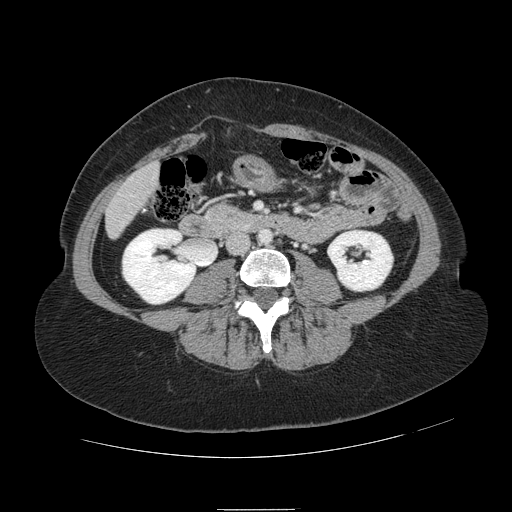
Contrast-enhanced abdominal CT, one axial slice. Position 10 of 121 along the scan axis. Intravenous contrast given. Soft-tissue window (W 400 / L 40 HU). 512 × 512 image matrix. Female patient, age 52 years. From the clinical record (not read from this slice): diagnosis: colorectal cancer liver metastases, imaged before liver resection; multiple liver metastases: yes; largest metastasis: 6.3 cm; disease in both lobes: no.
Structures marked on this image (expert manual segmentation):
- liver: bounding box <107,165,159,236> (left, top, right, bottom; pixels)